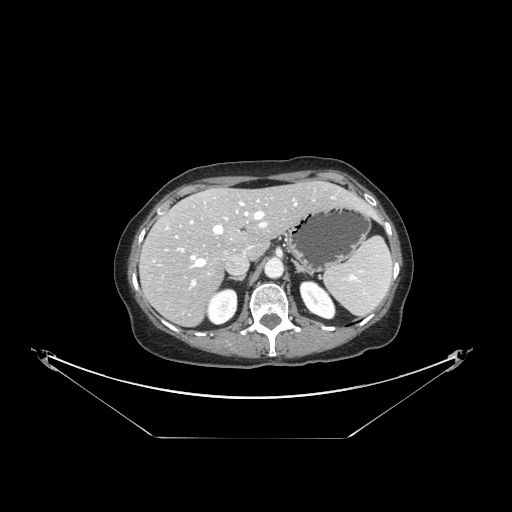
Contrast-enhanced abdominal CT, one axial slice. Position 100 of 148 along the scan axis. Reconstruction kernel STANDARD. 120 kVp. Soft-tissue window (W 400 / L 40 HU). 2.5 mm slice thickness. 512 × 512 image matrix. Female patient, age 73 years. From the clinical record (not read from this slice): diagnosis: colorectal cancer liver metastases, imaged before liver resection; multiple liver metastases: no.
Annotated regions visible in this slice (outlined manually by an expert reader):
- hepatic veins: box from (x=167, y=196) to (x=334, y=267) px
- liver: (x=142, y=182)–(x=370, y=326)
- planned liver remnant (the part of the liver to remain after resection): (x=168, y=182)–(x=369, y=257)
- portal vein (with intrahepatic branches): (x=175, y=210)–(x=267, y=287)